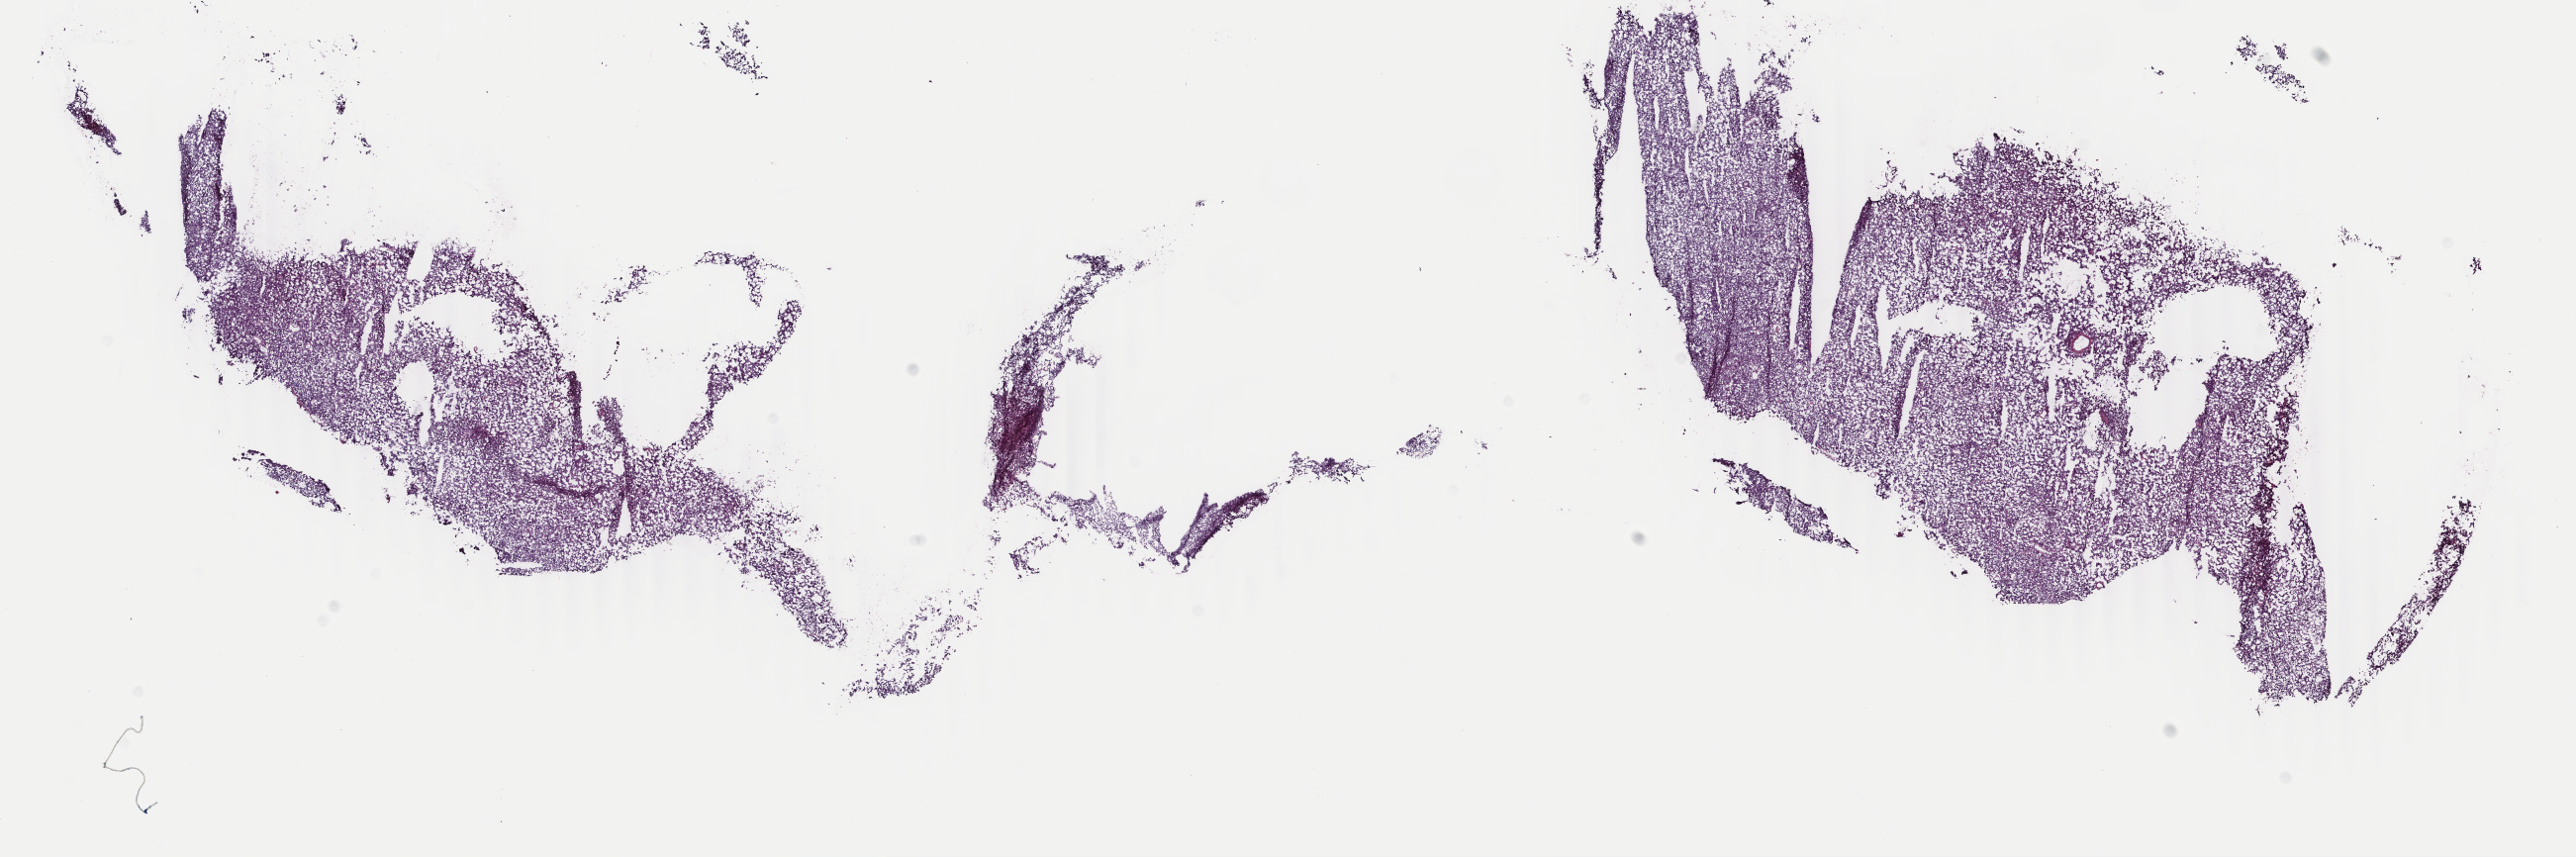
Hematoxylin and eosin (H&E) stained whole-slide image, a low-resolution overview of the entire scanned area, about 20.7 x 6.9 mm (acquisition: 40x scan), frozen section from the top of the tissue portion, primary tumour sample from the adrenal cortex. Male, age 57 years at initial diagnosis. Slide review estimates, as recorded: tumour cells 100%, tumour nuclei 95%, normal cells 0%, stromal cells 0%, necrosis 0%. Inflammatory infiltration, as recorded: lymphocyte infiltration 0%, monocyte infiltration 0%, neutrophil infiltration 0%.
Diagnosis: Adrenal cortical carcinoma (cortex of adrenal gland). Lymph nodes positive (case pathology): 0 of 18 examined.